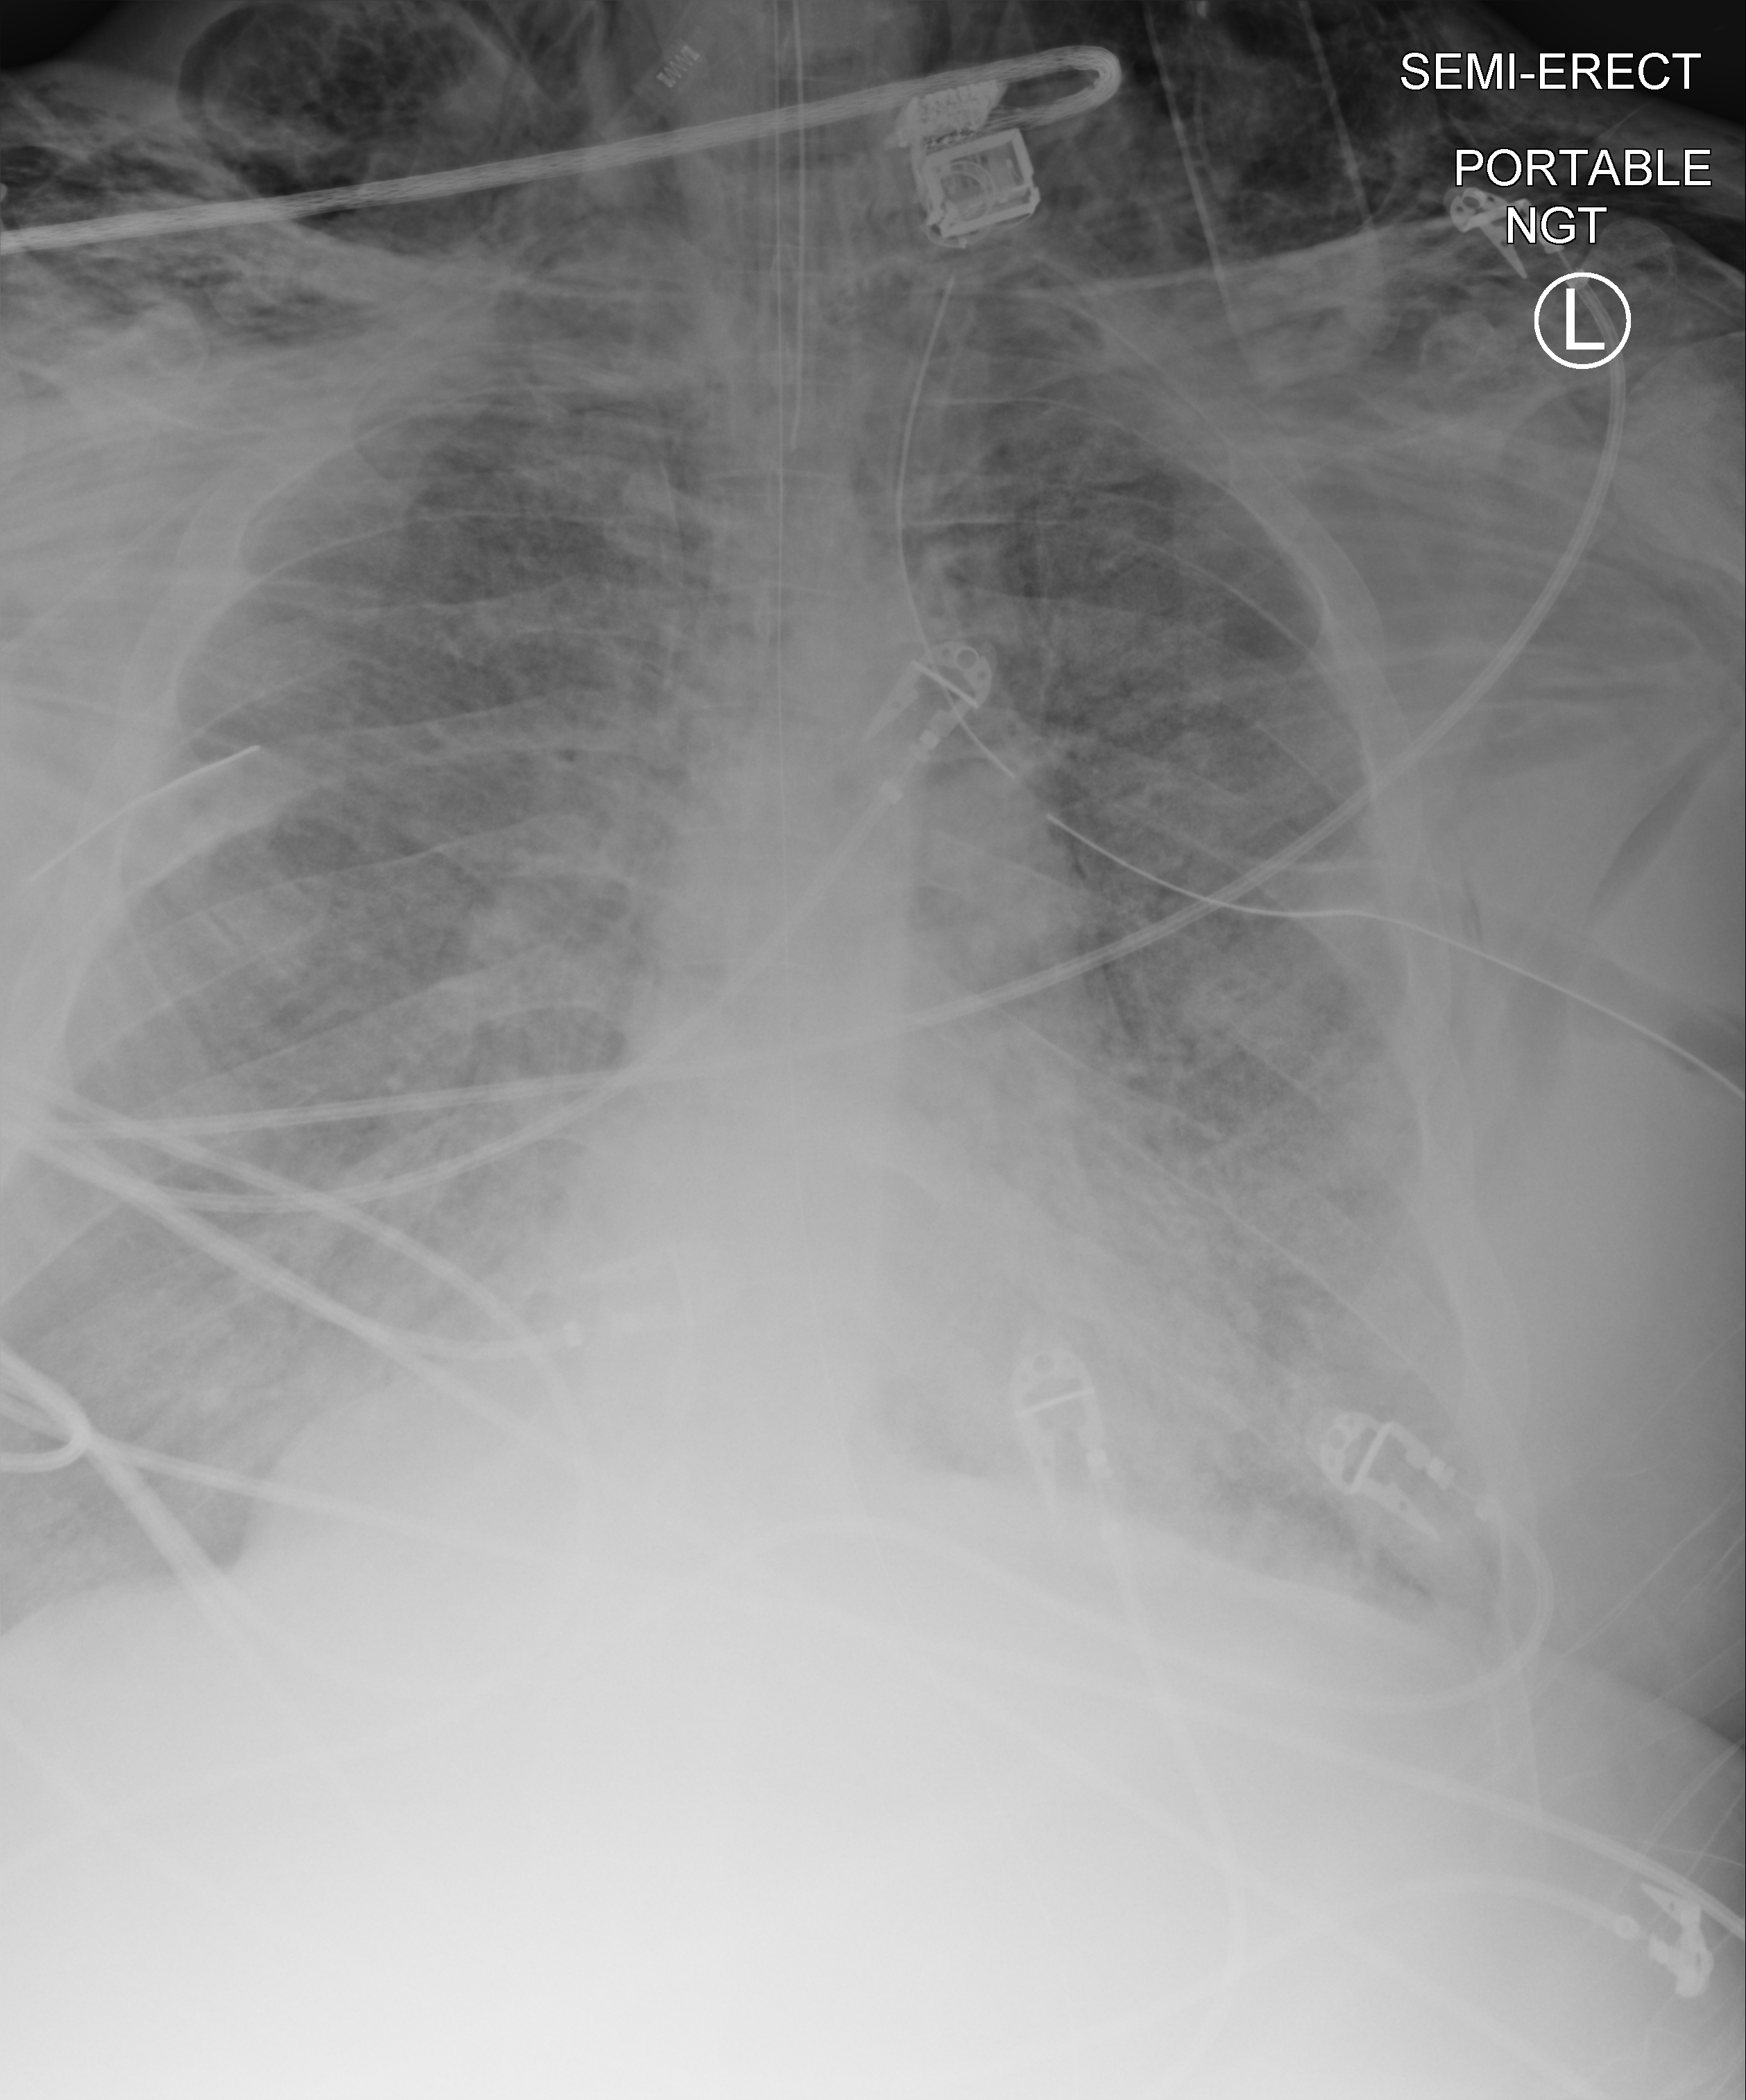
Portable chest radiograph, anteroposterior (AP) projection. Patient hospitalised with COVID-19, aged 18–59 years.
Admission-level facts for this patient (not findings on this image; timing relative to this image not recorded):
- admitted to intensive care during this hospital stay: yes
- mechanically ventilated during this hospital stay: yes